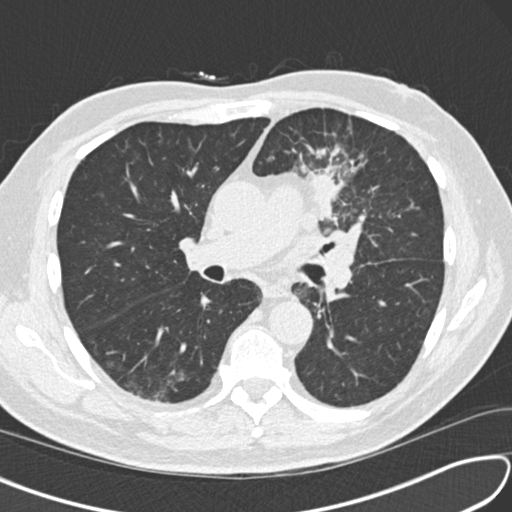
Low-dose screening chest CT, one axial slice; position 87 of 156 along the scan axis; reconstruction kernel B30f; lung window (W 1500 / L -600 HU); 2 mm slice thickness; 512 × 512 image matrix, field of view 340 × 340 mm.
Structures marked on this image (manually delineated by an expert):
- lesion 1 (tumor, upper lobe of left lung): bounding box <308,168,341,220> (left, top, right, bottom; pixels)